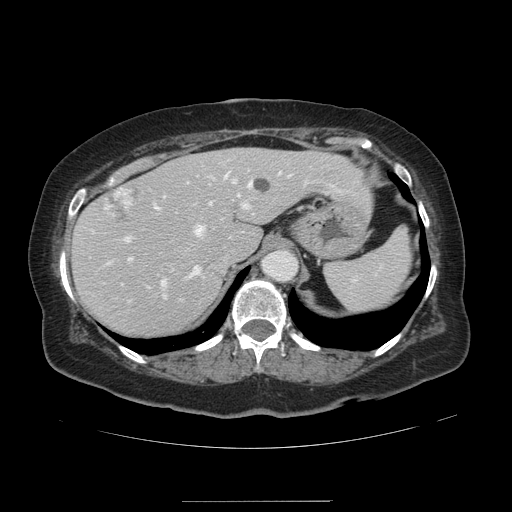
Contrast-enhanced abdominal CT, one axial slice. Position 96 of 141 along the scan axis. Soft-tissue window (W 400 / L 40 HU). 2.5 mm slice thickness. 512 × 512 image matrix, field of view 393 × 393 mm. Female patient, age 74 years. From the clinical record (not read from this slice): diagnosis: colorectal cancer liver metastases, imaged before liver resection; multiple liver metastases: yes; largest metastasis: 7 cm; chemotherapy before resection: no.
Annotated regions visible in this slice (outlined manually by an expert reader):
- hepatic veins: bounding box <153,172,280,279> (left, top, right, bottom; pixels)
- liver: <74,148,370,339>
- planned liver remnant (the part of the liver to remain after resection): <74,148,370,339>
- portal vein (with intrahepatic branches): <125,173,329,300>
- liver metastasis: <252,177,272,193>
- liver metastasis: <96,186,137,226>
- liver metastasis: <142,337,151,339>